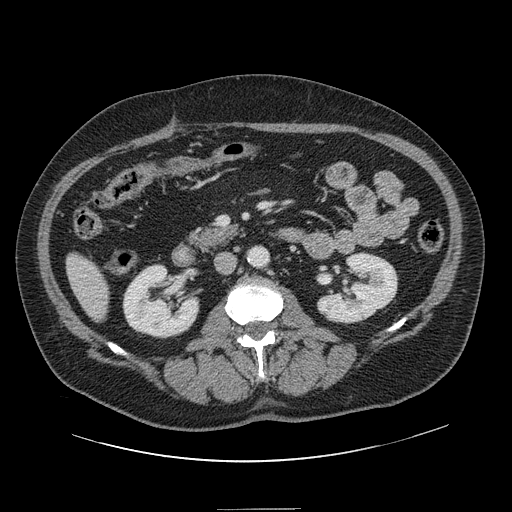
Contrast-enhanced abdominal CT, one axial slice. Slice 40 of 154 in the series (ordered by position). 120 kVp. Intravenous contrast given. Soft-tissue window (W 400 / L 40 HU). 512 × 512 image matrix, field of view 451 × 451 mm. Male patient, age 61 years. Case-level facts recorded for this patient, not image findings: diagnosis: colorectal cancer liver metastases, imaged before liver resection; multiple liver metastases: yes; largest metastasis: 2.6 cm.
Annotated regions visible in this slice (expert manual segmentation):
- liver: bounding box <68,254,109,320> (left, top, right, bottom; pixels)
- planned liver remnant (the part of the liver to remain after resection): <67,254,109,320>